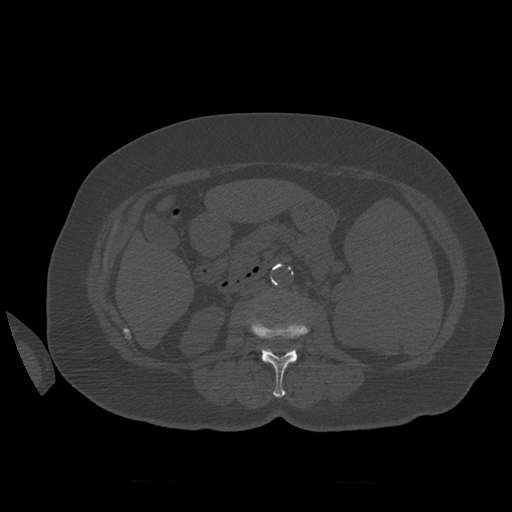
CT including the spine, one axial slice. Slice 247 of 399 in the series (ordered by position). Reconstruction kernel STANDARD. Bone window (W 1800 / L 400 HU). 1.25 mm slice thickness. 512 × 512 image matrix, field of view 404 × 404 mm. Patient age 81 years. Case-level facts recorded for this patient, not image findings: primary cancer: renal; vertebrae with lytic lesions (as recorded): L1.
Structures marked on this image (semi-automatic segmentation, software-assisted and operator-edited):
- L2 vertebra: bounding box (x1, y1, x2, y2) in pixels: (250, 319, 310, 398)